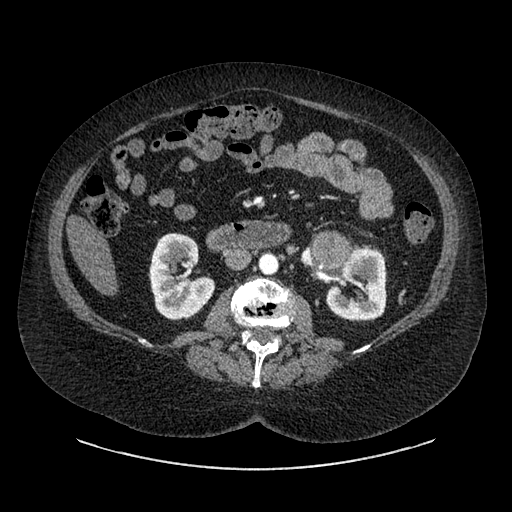
Contrast-enhanced abdominal CT, one axial slice; slice 489 of 769 in the series (ordered by position); reconstruction kernel SOFT; 120 kVp; intravenous contrast given; soft-tissue window (W 400 / L 40 HU); 512 × 512 image matrix, field of view 460 × 460 mm. Patient: female, 61 years. From the clinical record (not read from this slice): diagnosis: adrenocortical carcinoma; tumour side: left adrenal; tumour size at pathology: 13 cm; Ki-67 index: 79 %; stage (as recorded): 2.
Outlined on this slice (semi-automatically segmented with operator editing):
- mass: box from (x=316, y=238) to (x=344, y=266) px